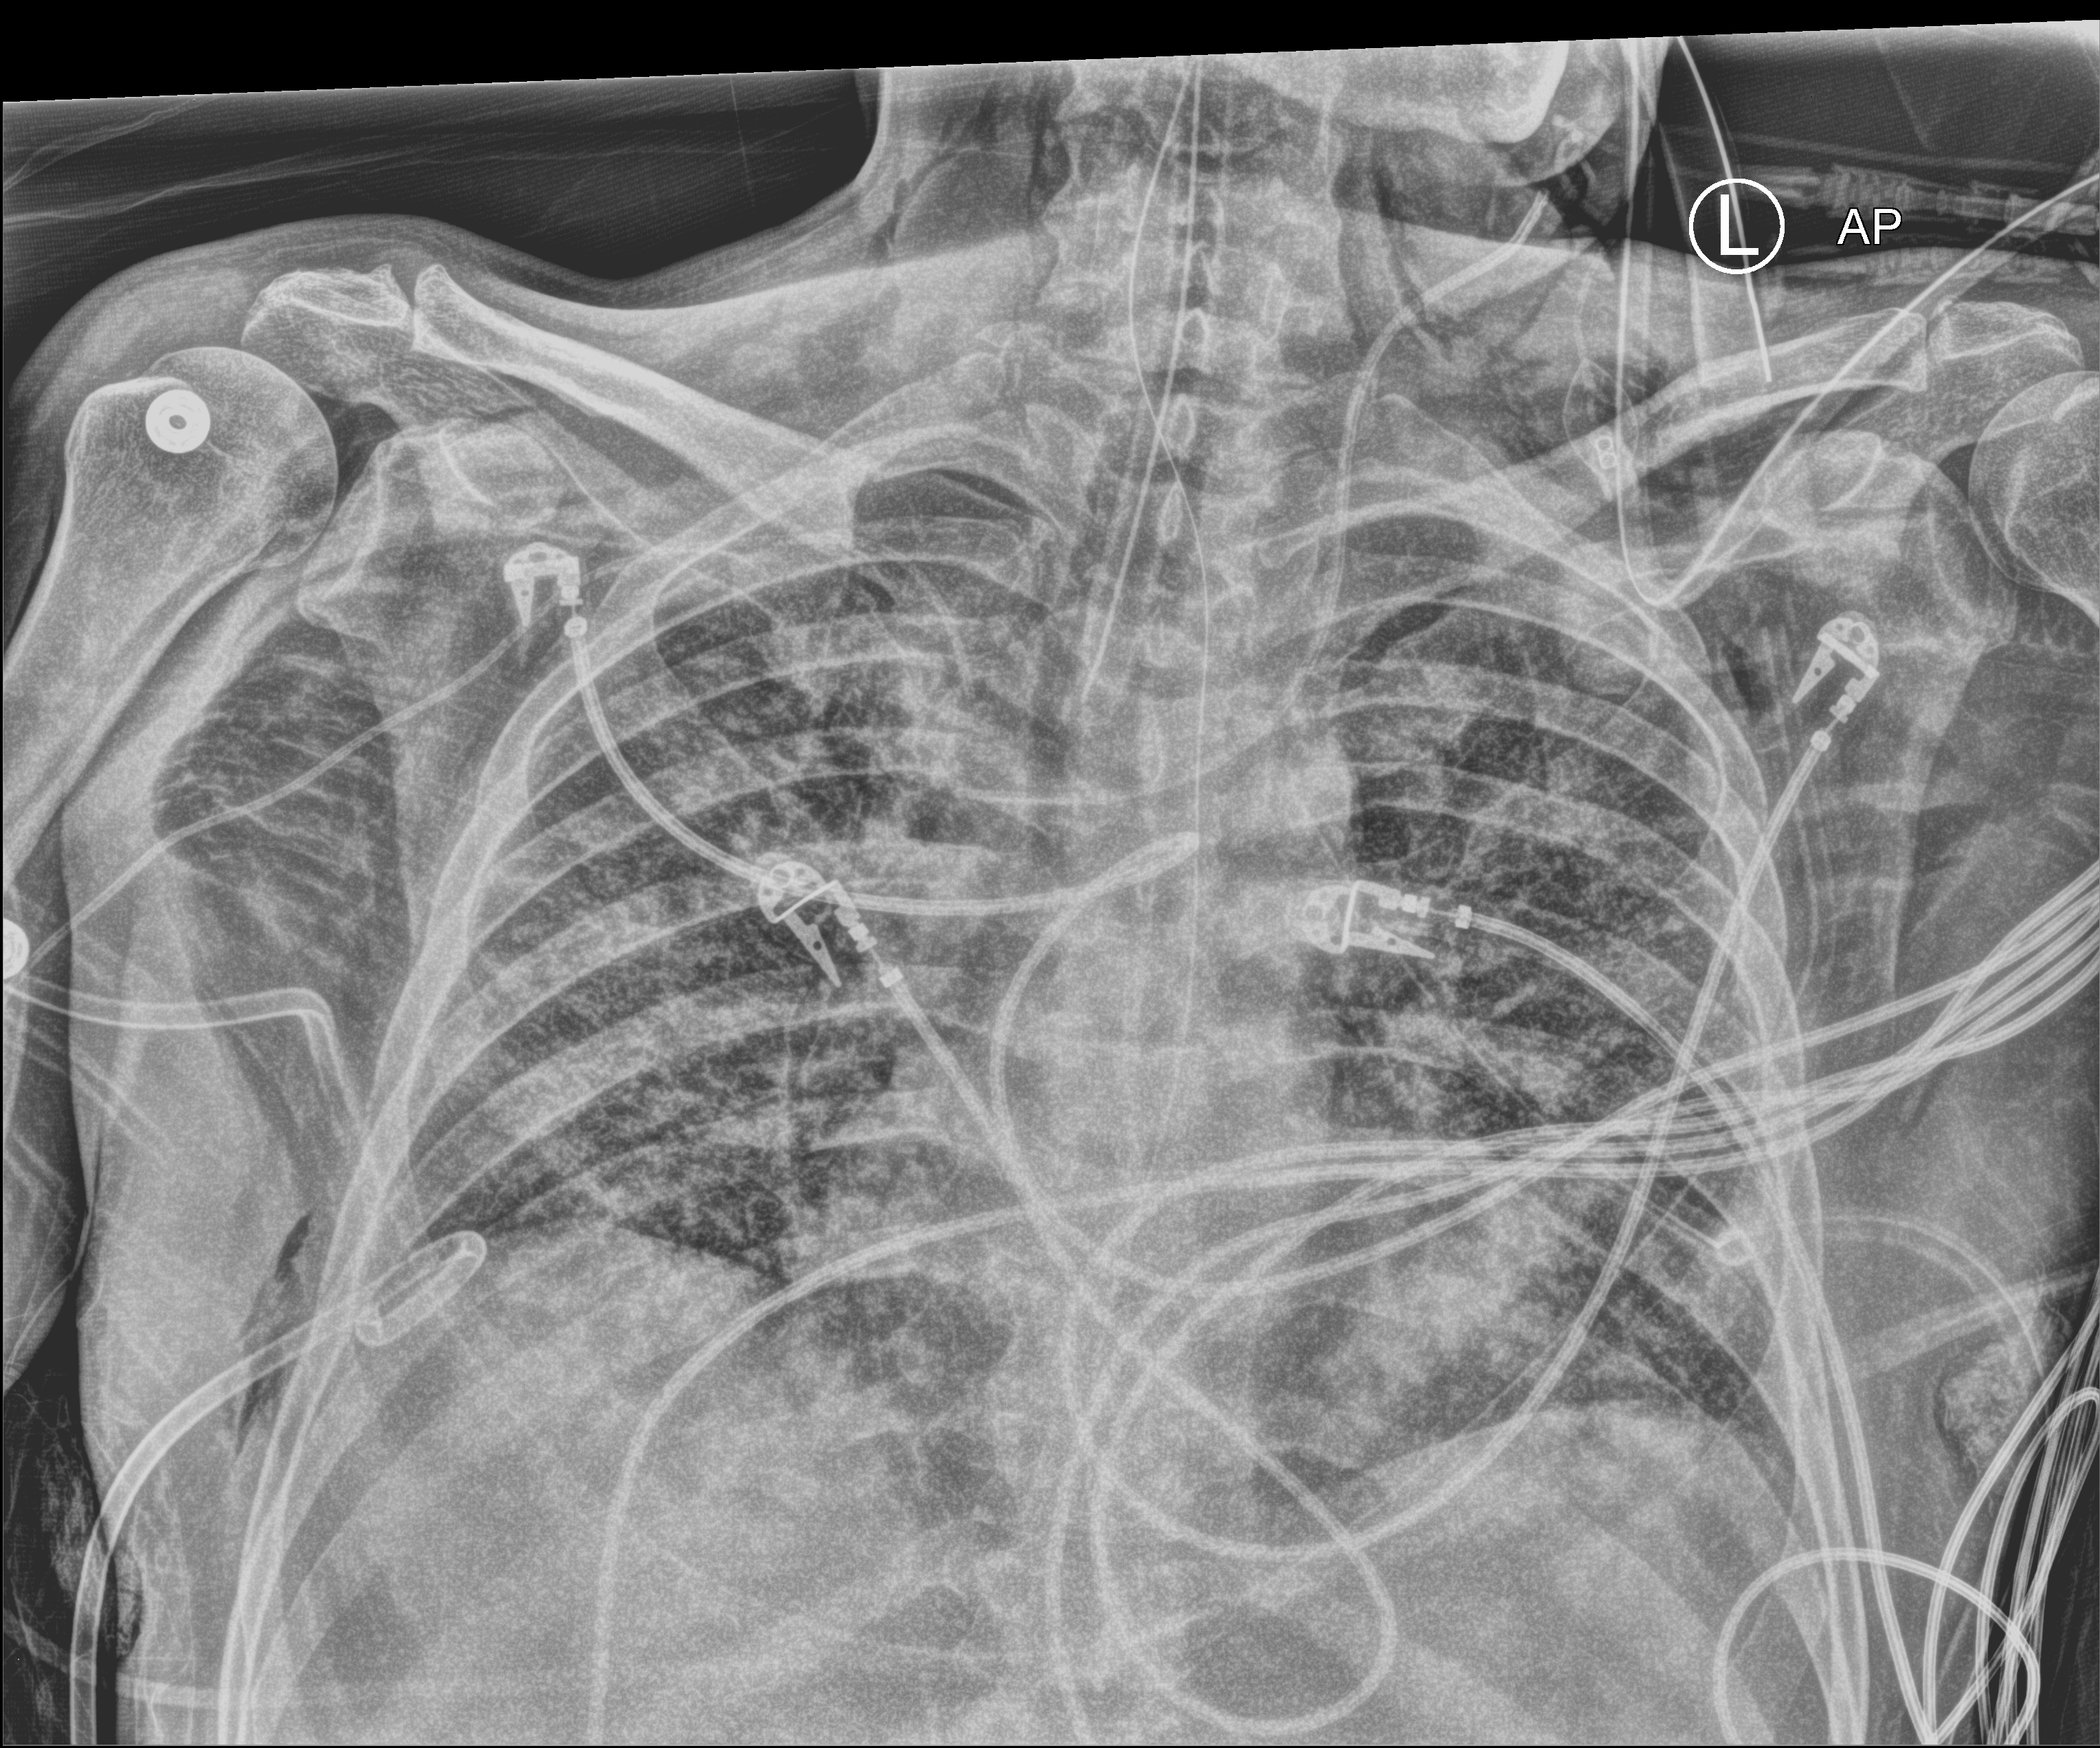
Bedside chest radiograph (computed radiography), anteroposterior (AP) projection. Patient hospitalised with COVID-19; male, aged 18–59 years.
Hospital-stay facts (about this admission, not read from this image; timing relative to this image not recorded): admitted to intensive care during this hospital stay: yes; hypertension (admission record): no; mechanically ventilated during this hospital stay: yes.